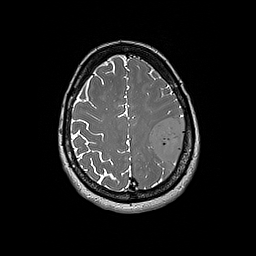
Brain MRI from a brain-tumour surgery series, one axial slice. Slice 61 of 192 in the series (ordered by position). 1 mm slice thickness. 256 × 256 image matrix, field of view 250 × 250 mm. From the clinical record (not read from this slice): histopathology: Glioblastoma; WHO grade: 4; IDH mutation: no; tumour location: Left Frontal.
Annotated regions visible in this slice (expert manual segmentation):
- tumour: bounding box <150,114,186,164> (left, top, right, bottom; pixels)